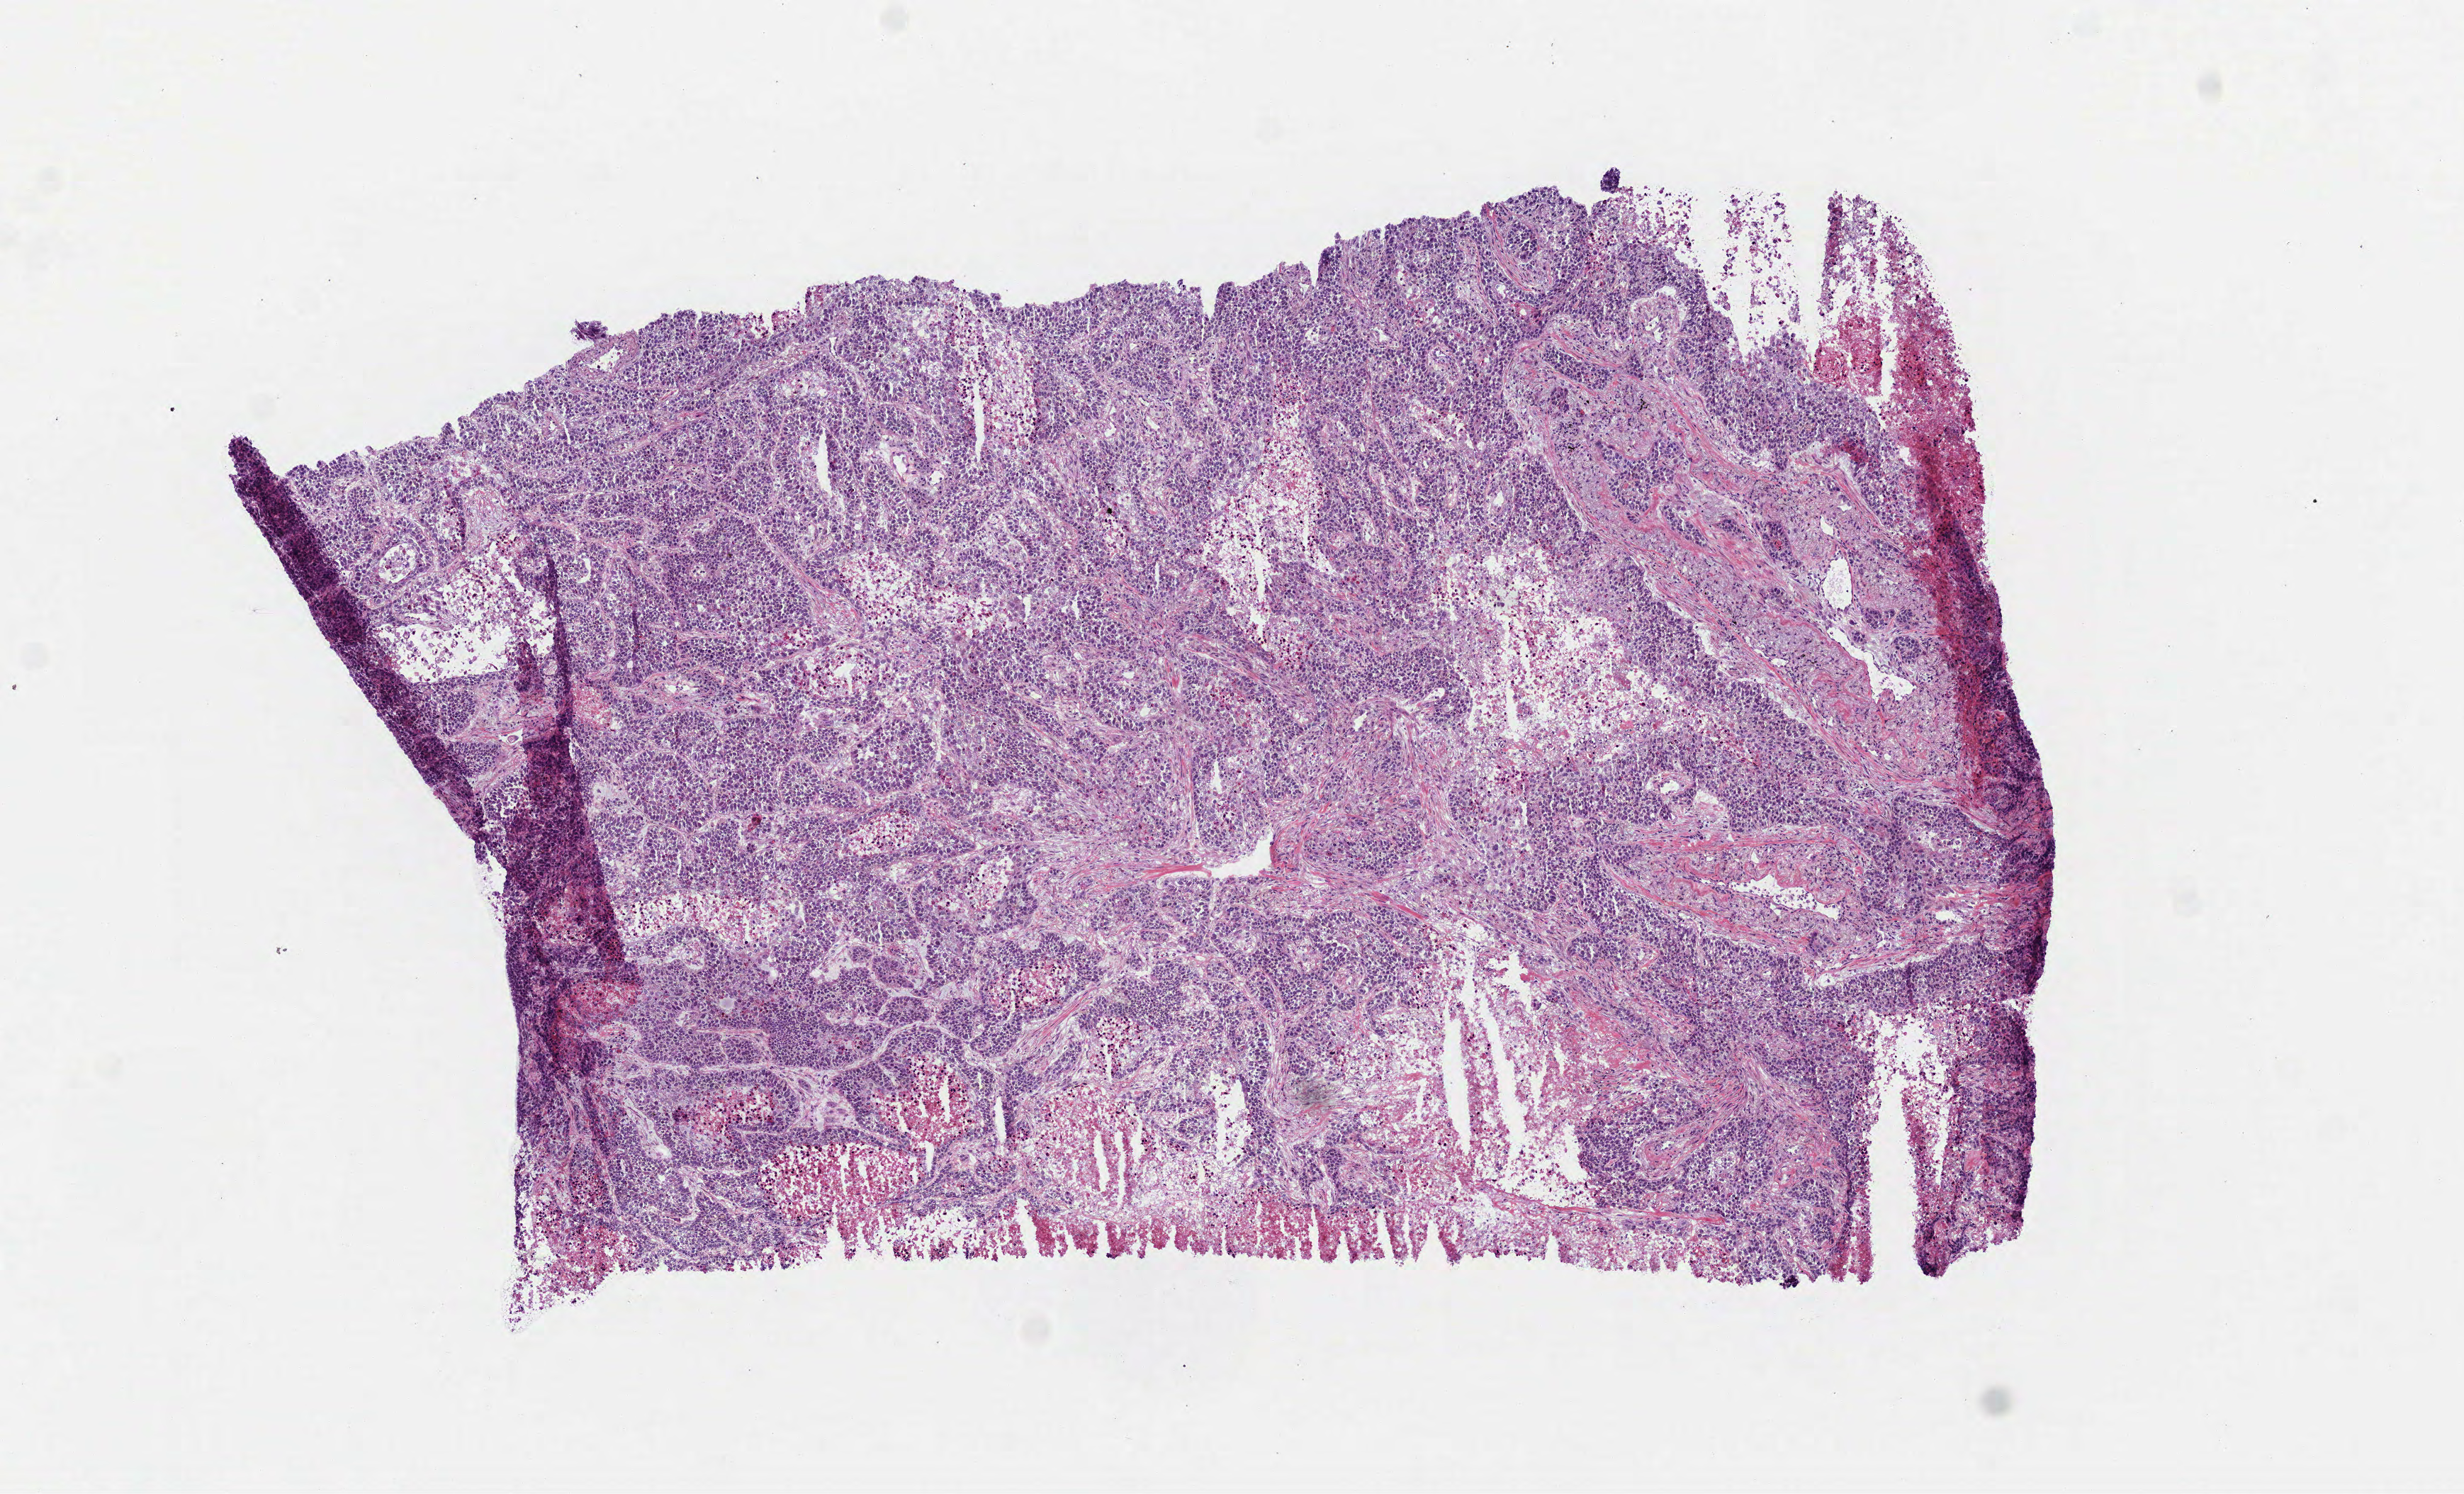
H&E whole-slide image, a low-resolution overview of the entire scanned area, about 7.0 x 4.3 mm; frozen section from the bottom of the tissue portion; primary tumour sample from the lung. Patient: male, age at initial diagnosis 81 years. Composition of this section per pathologist review: tumour cells 65%, tumour nuclei 80%, normal cells 0%, stromal cells 10%, necrosis 25%.
- pathologic diagnosis: Squamous cell carcinoma, NOS (lower lobe, lung)
- AJCC pathologic stage: IIB
- laterality: right